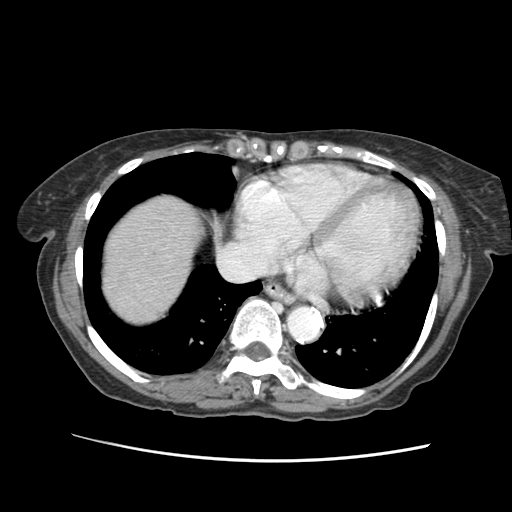
Contrast-enhanced abdominal CT (liver protocol), one axial slice; position 56 of 63 along the scan axis; 120 kVp; soft-tissue window (W 400 / L 40 HU); 2.5 mm slice thickness; 512 × 512 image matrix, field of view 340 × 340 mm. From the clinical record (not read from this slice): diagnosis: hepatocellular carcinoma (patient treated with transarterial chemoembolisation; whether this scan precedes or follows treatment is not stated here); TNM stage (as recorded): Stage-I; Child-Pugh class: B; tumour differentiation: well differentiated; tumour nodularity: uninodular.
Structures marked on this image (semi-automatically segmented with operator editing):
- liver parenchyma outside the tumour (the mass and vessels are separate outlines, so this box may not span the whole liver): bounding box [x1, y1, x2, y2] px = [106, 196, 196, 313]